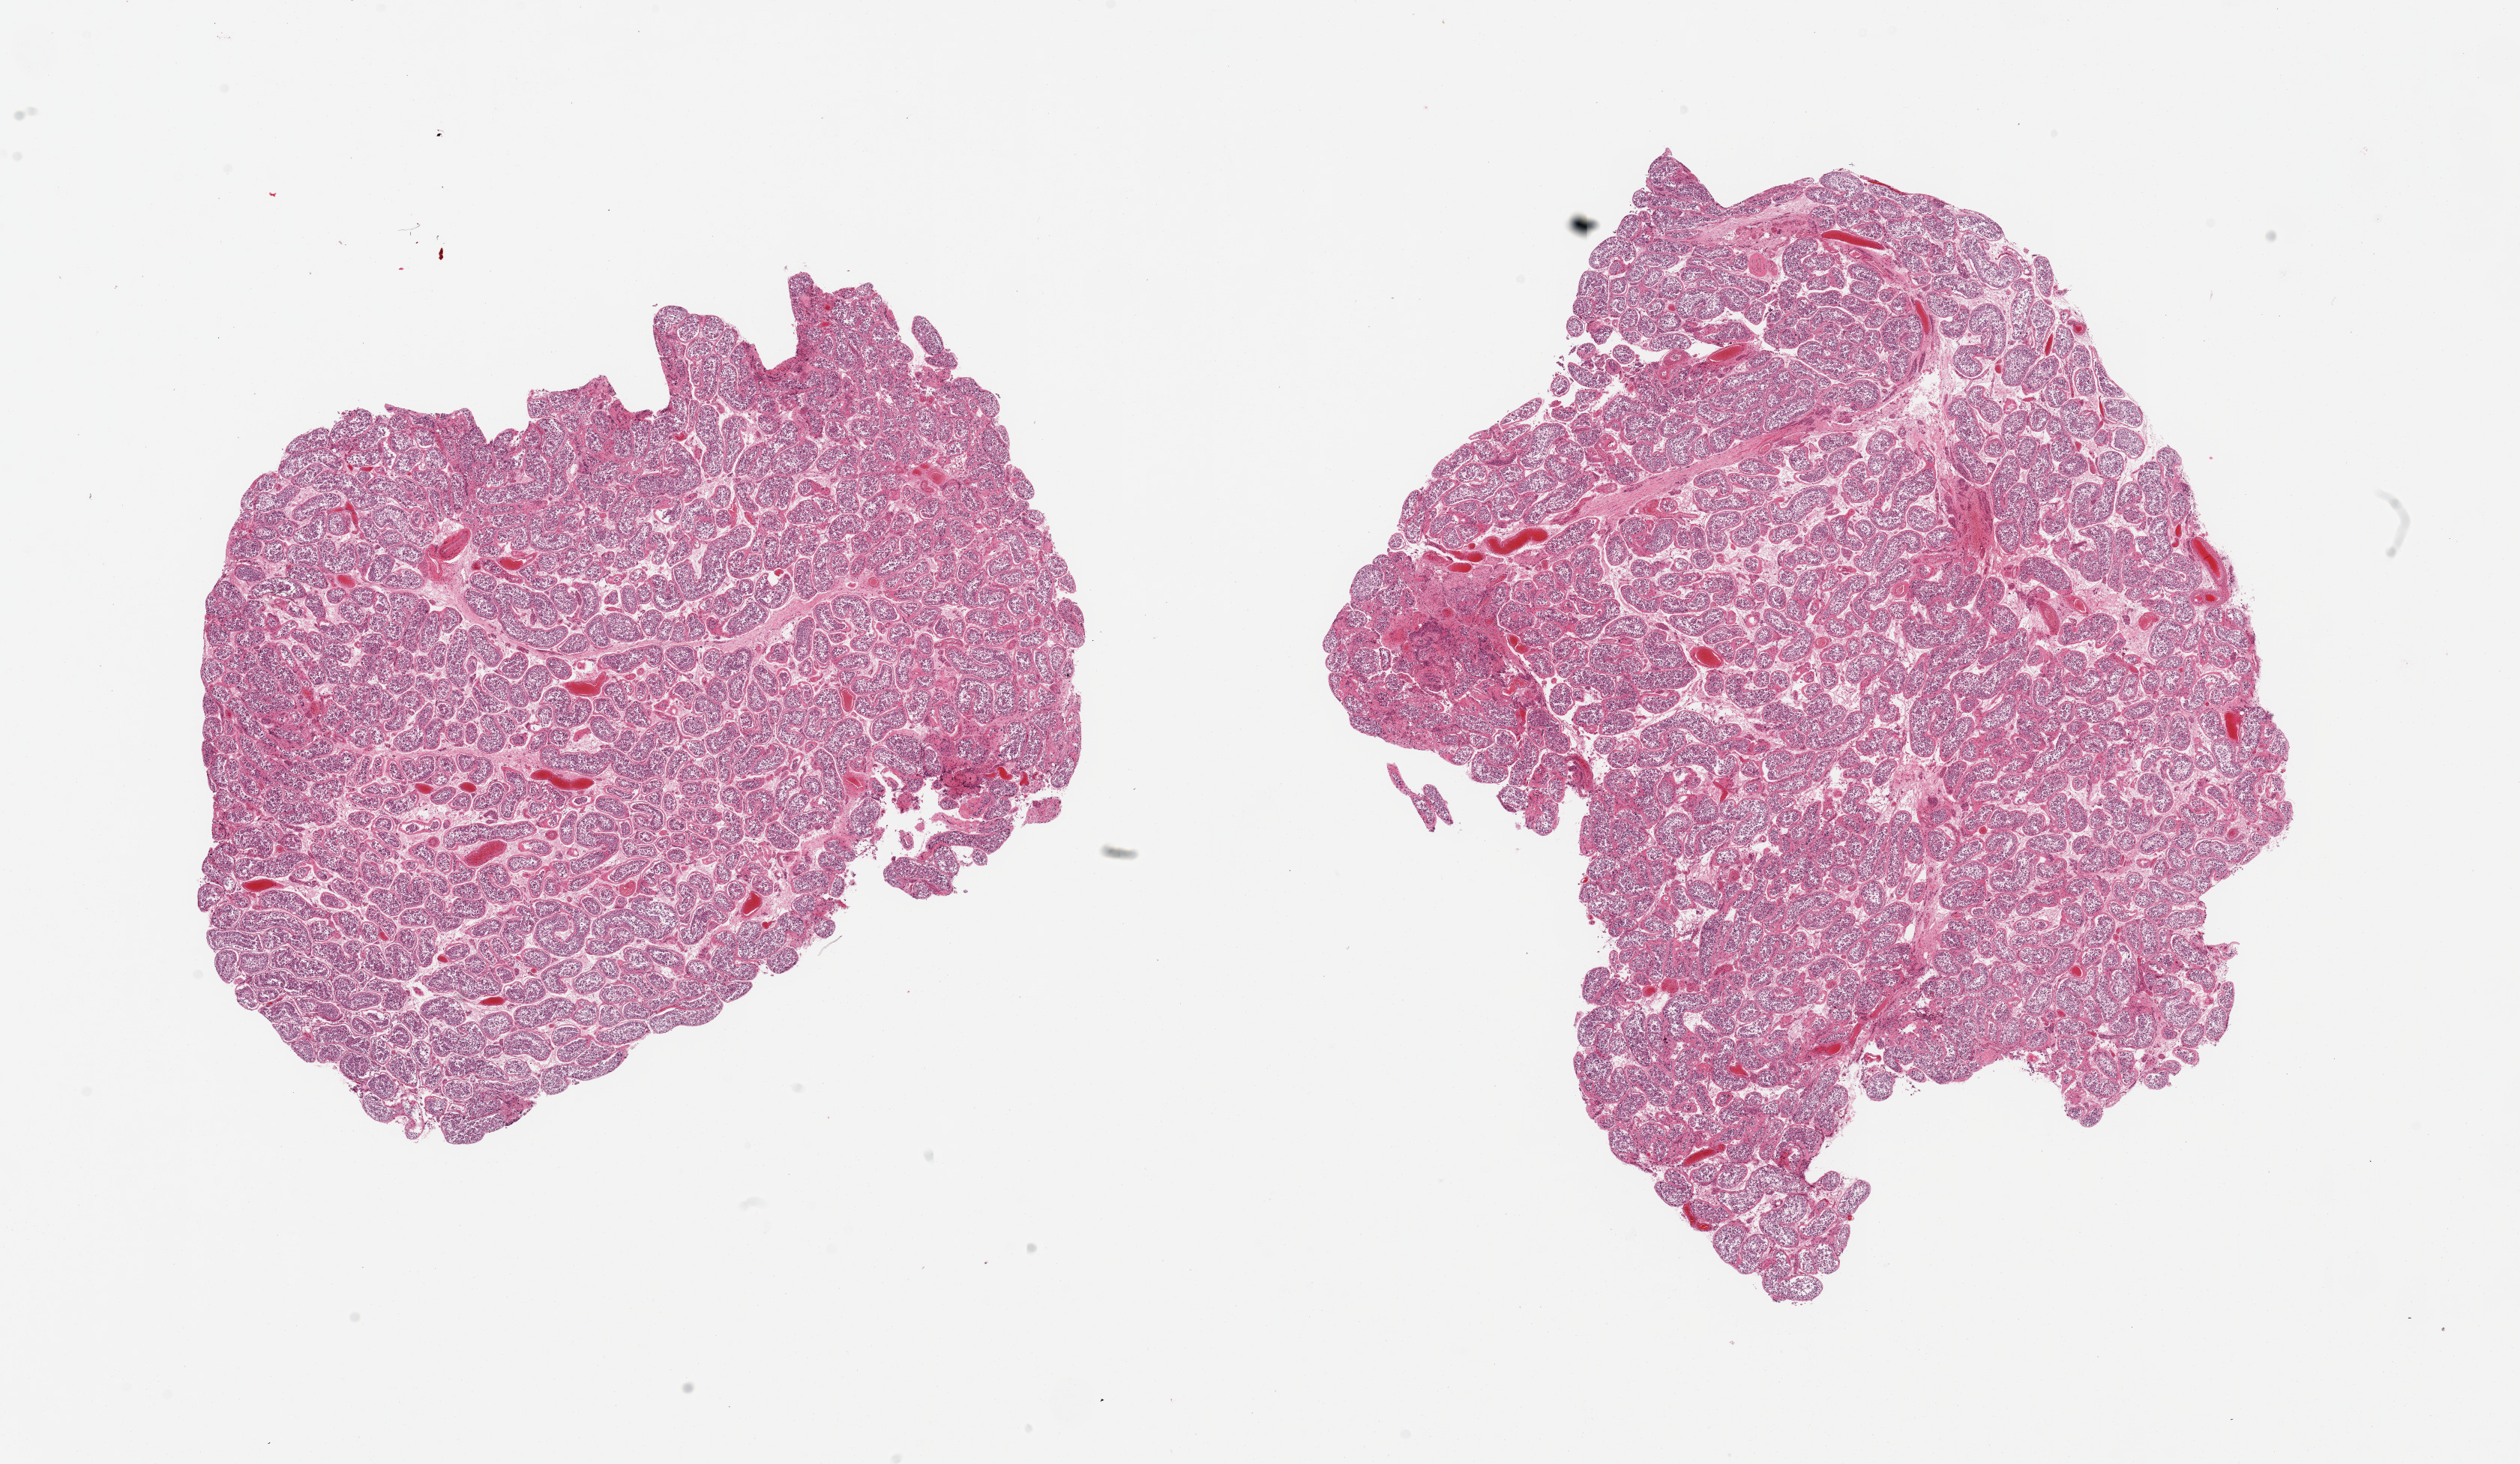
Whole-slide image, hematoxylin and eosin (H&E) stain — low-resolution overview of the scanned area, about 26.6 x 15.4 mm (from a 20x scan), PAXgene-fixed, paraffin-embedded tissue, section of testis (target tissue), donor tissue sample.
Pathologist's review note for this sample: 2 pieces; active spermatogenesis.